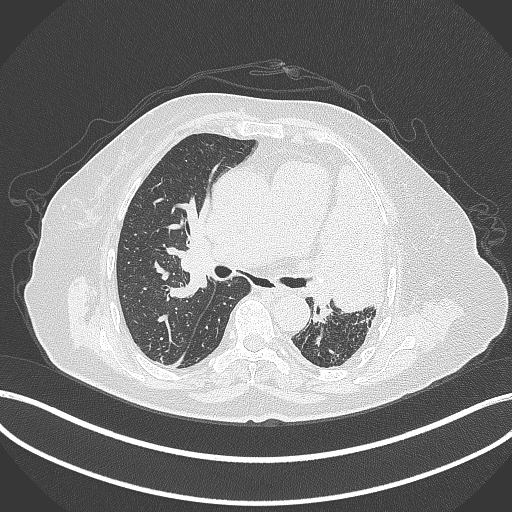
Chest CT, one axial slice; slice 226 of 399 in the series (ordered by position); lung window (W 1500 / L -600 HU); 512 × 512 image matrix, field of view 400 × 400 mm. Patient: female, 75 years. Case-level facts recorded for this patient, not image findings: clinical TNM (as recorded): T3 N3 M1.
Structures marked on this image (bounding box drawn by a radiologist):
- lung tumour (recorded histology: adenocarcinoma): bounding box [x1, y1, x2, y2] px = [310, 161, 394, 315]